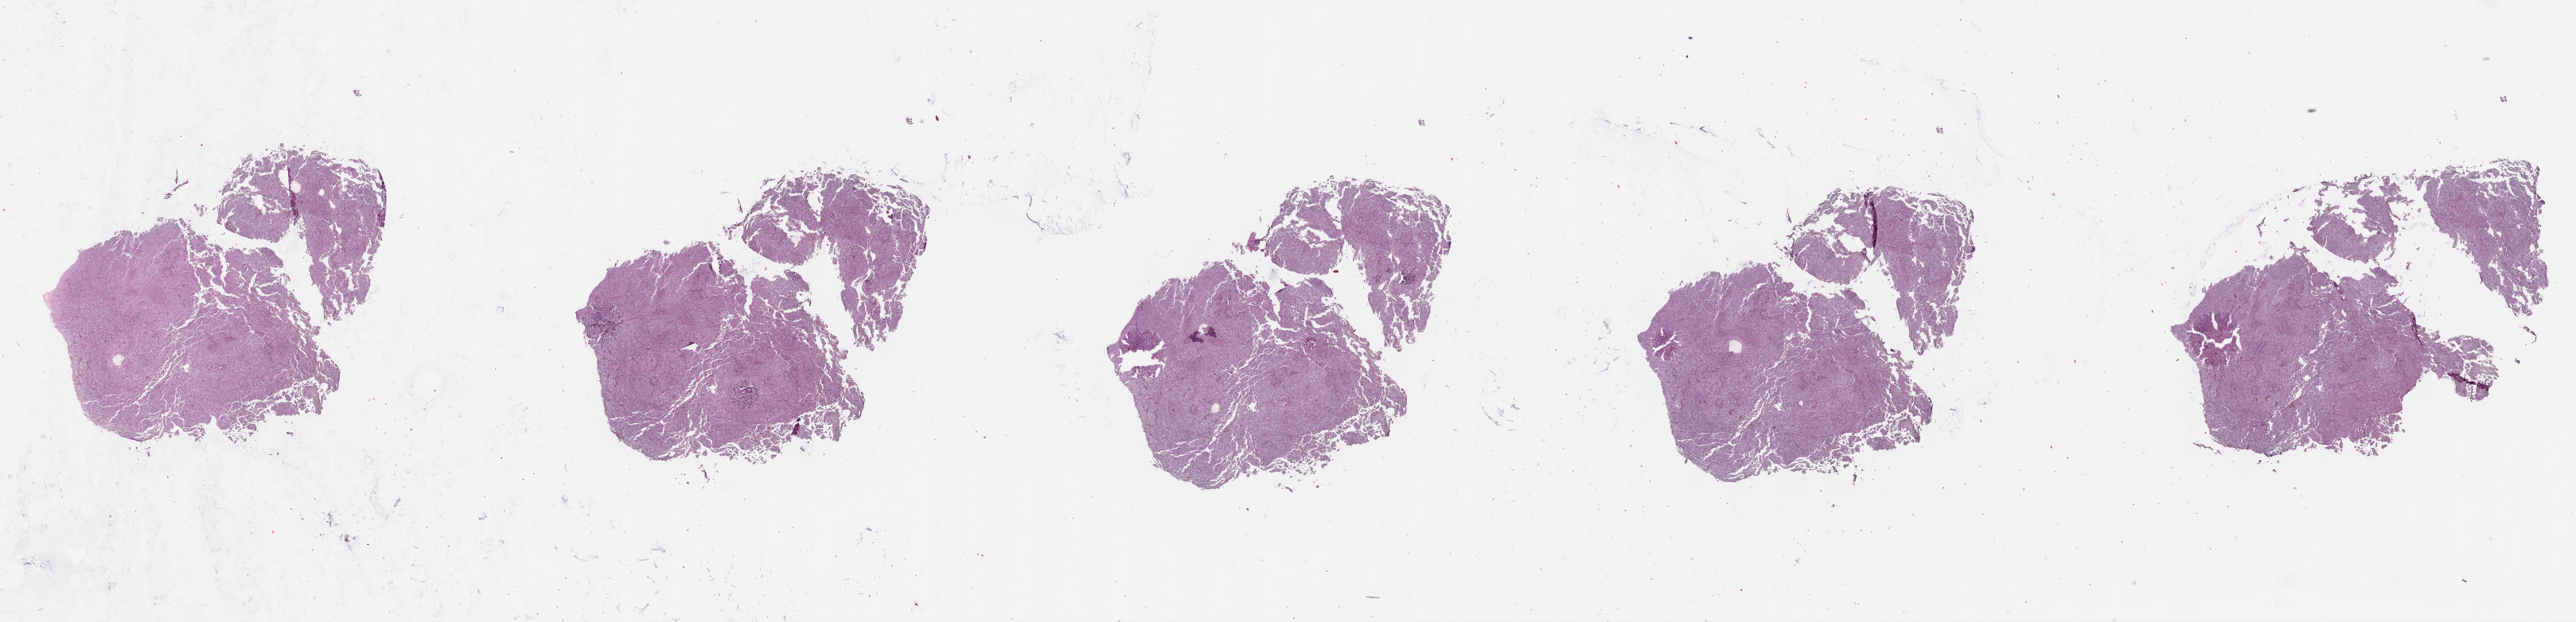
Whole-slide histology image, Hematoxylin and eosin (H&E) stained — shown as a low-resolution overview of the whole scanned area (about 52.1 x 12.6 mm). Female, 70 y/o.
Patient diagnosis: Malignant melanoma, NOS.